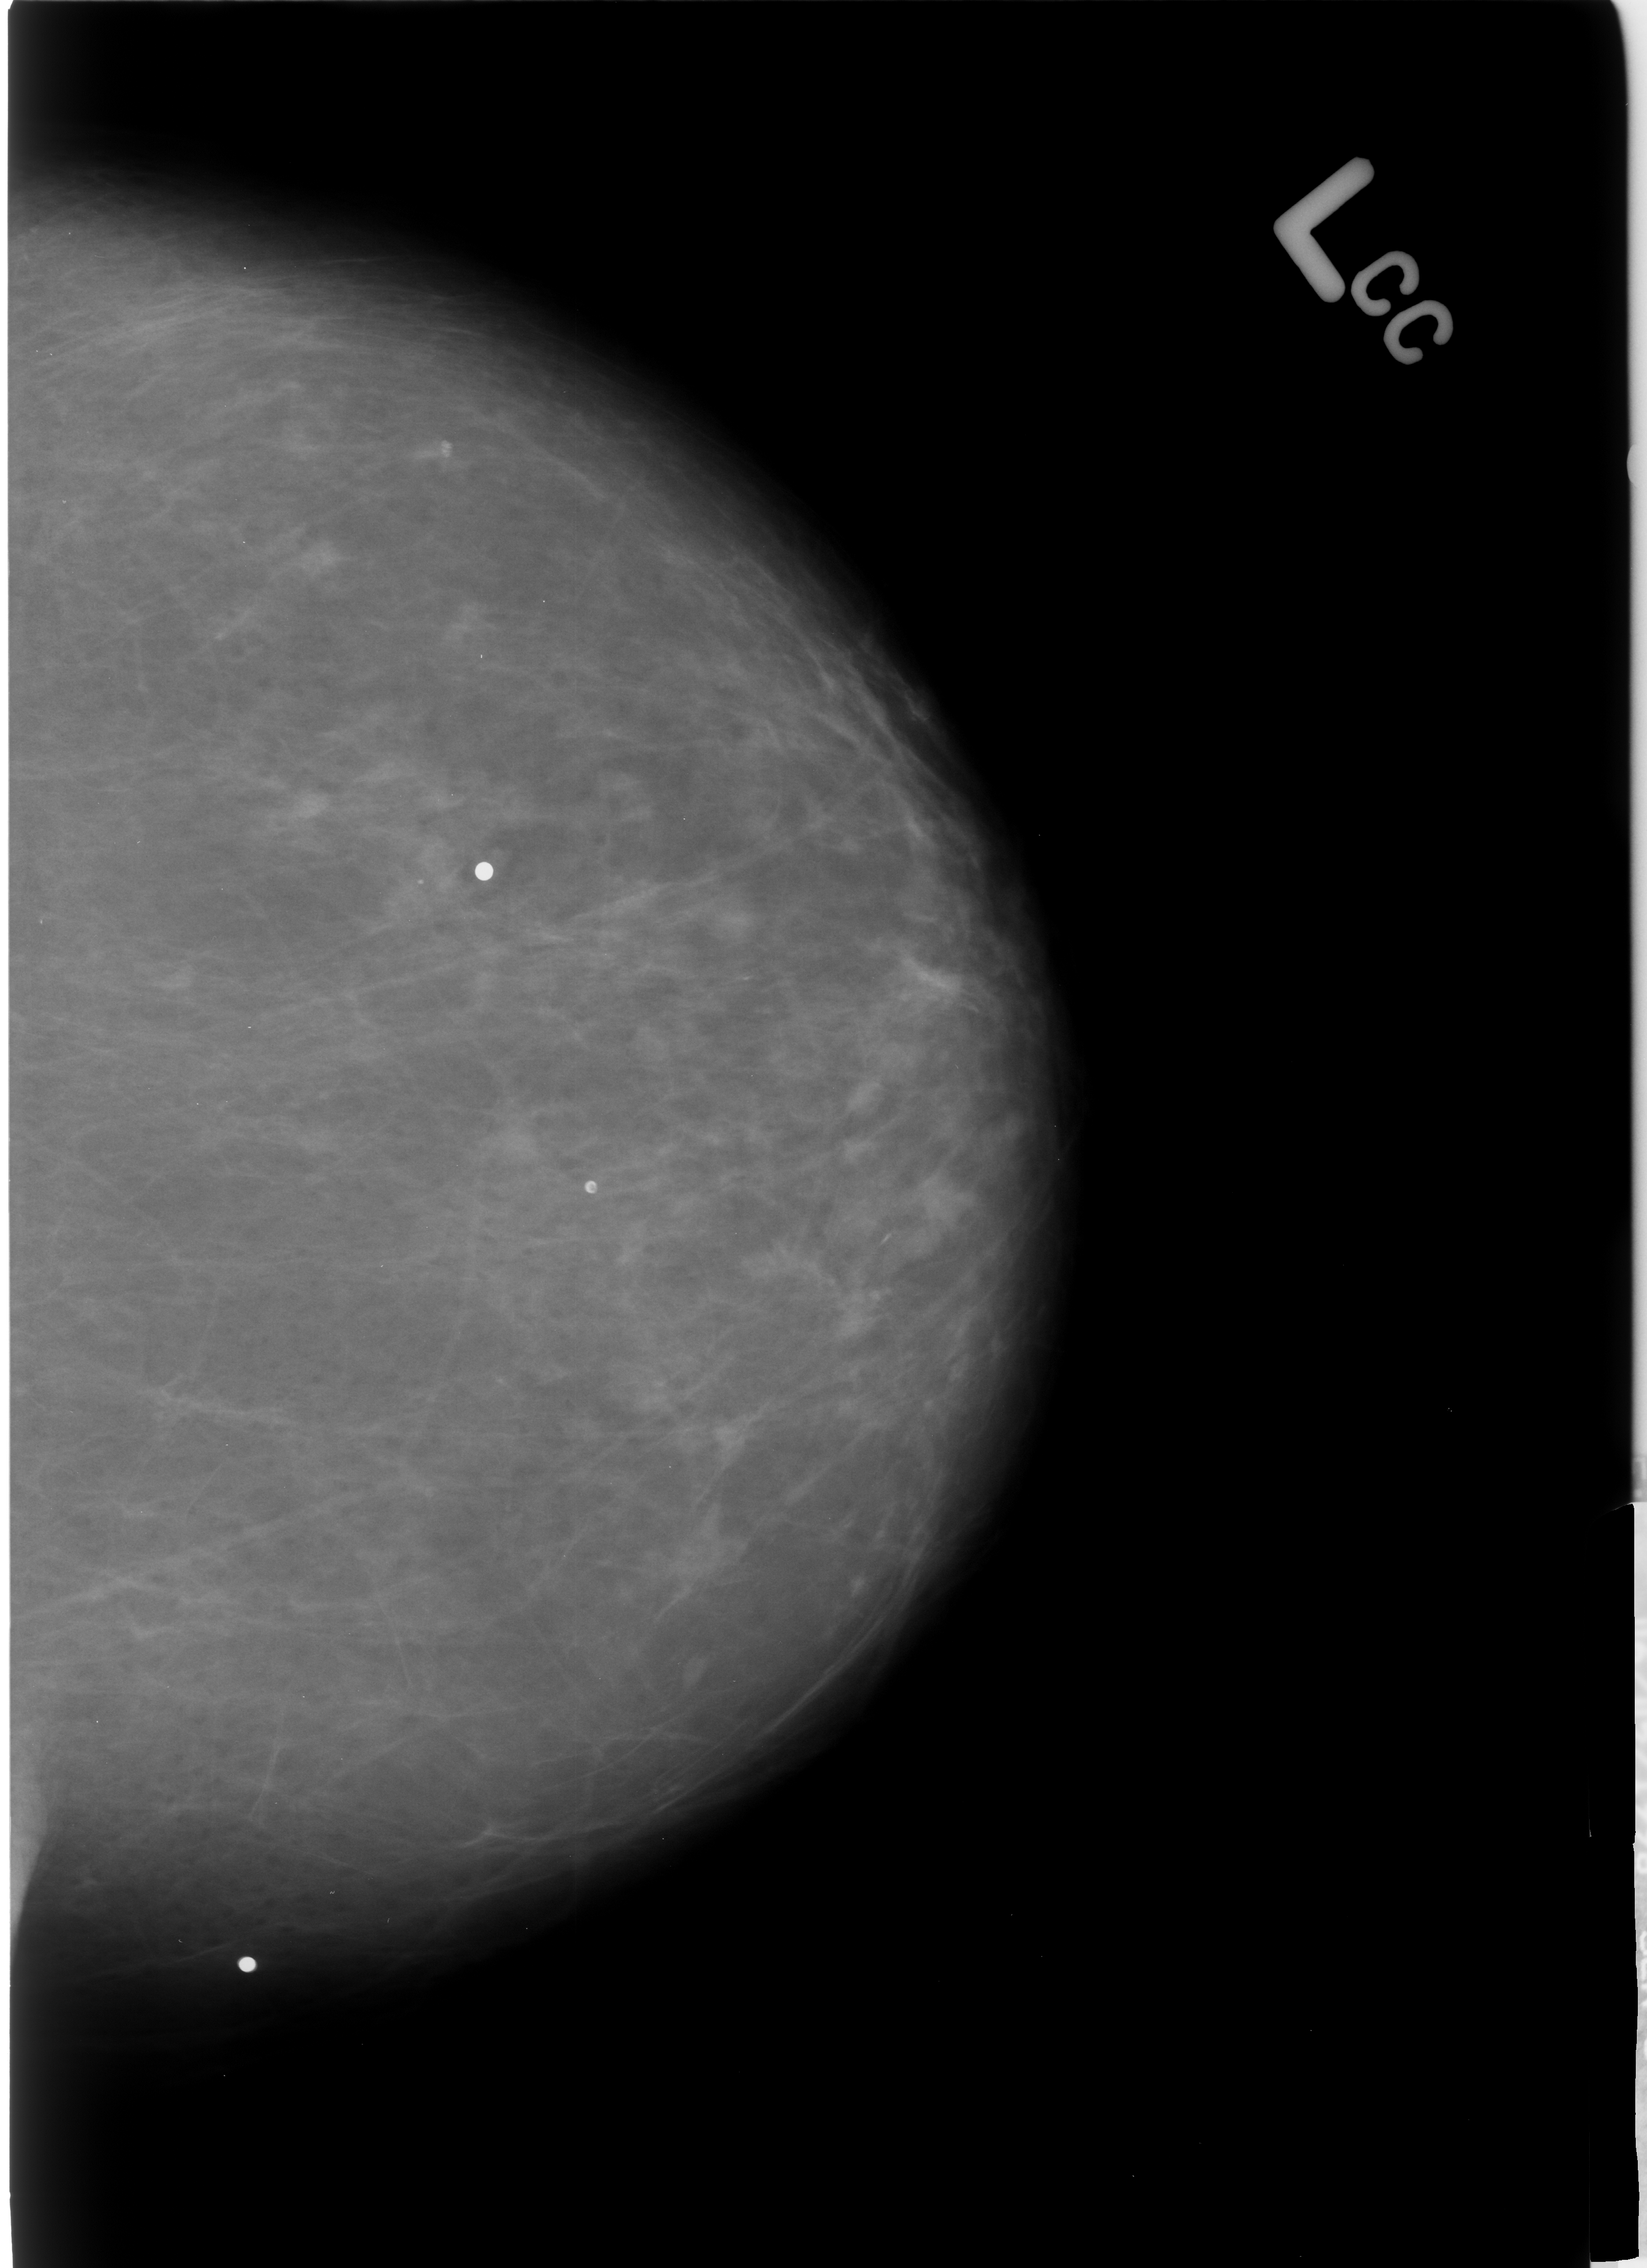
Mammogram (digitized film), left breast, craniocaudal (CC) view, breast composition: almost entirely fatty (BI-RADS density category 1 of 4).
Calcifications, morphology lucent center; BI-RADS assessment category 2; benign without callback (not worked up further).